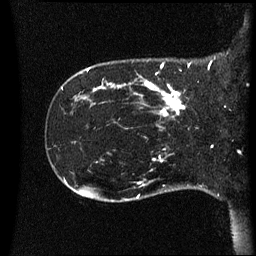
Breast MRI (dynamic contrast-enhanced), one sagittal slice. Slice 11 of 60 in the series (ordered by position). Dynamic contrast-enhanced series, image 2 of 3 at this slice position (ordered by acquisition). 1.5 T. TE 4.2 ms, TR 8.4 ms. 2.2 mm slice thickness. 256 × 256 image matrix. Female patient, age 41 years. Case-level facts recorded for this patient, not image findings: setting: breast cancer imaged before/during neoadjuvant chemotherapy; receptor status: HER2-positive.
Annotated regions visible in this slice (semi-automatic segmentation, software-assisted and operator-edited):
- analysis volume of interest (the breast-tissue region the enhancement analysis was run in; not a lesion): bounding box (x1, y1, x2, y2) in pixels: (122, 80, 190, 123)
- tumour enhancement mask (voxels above the 70 % enhancement threshold inside the analysis volume of interest): (145, 80, 186, 117)